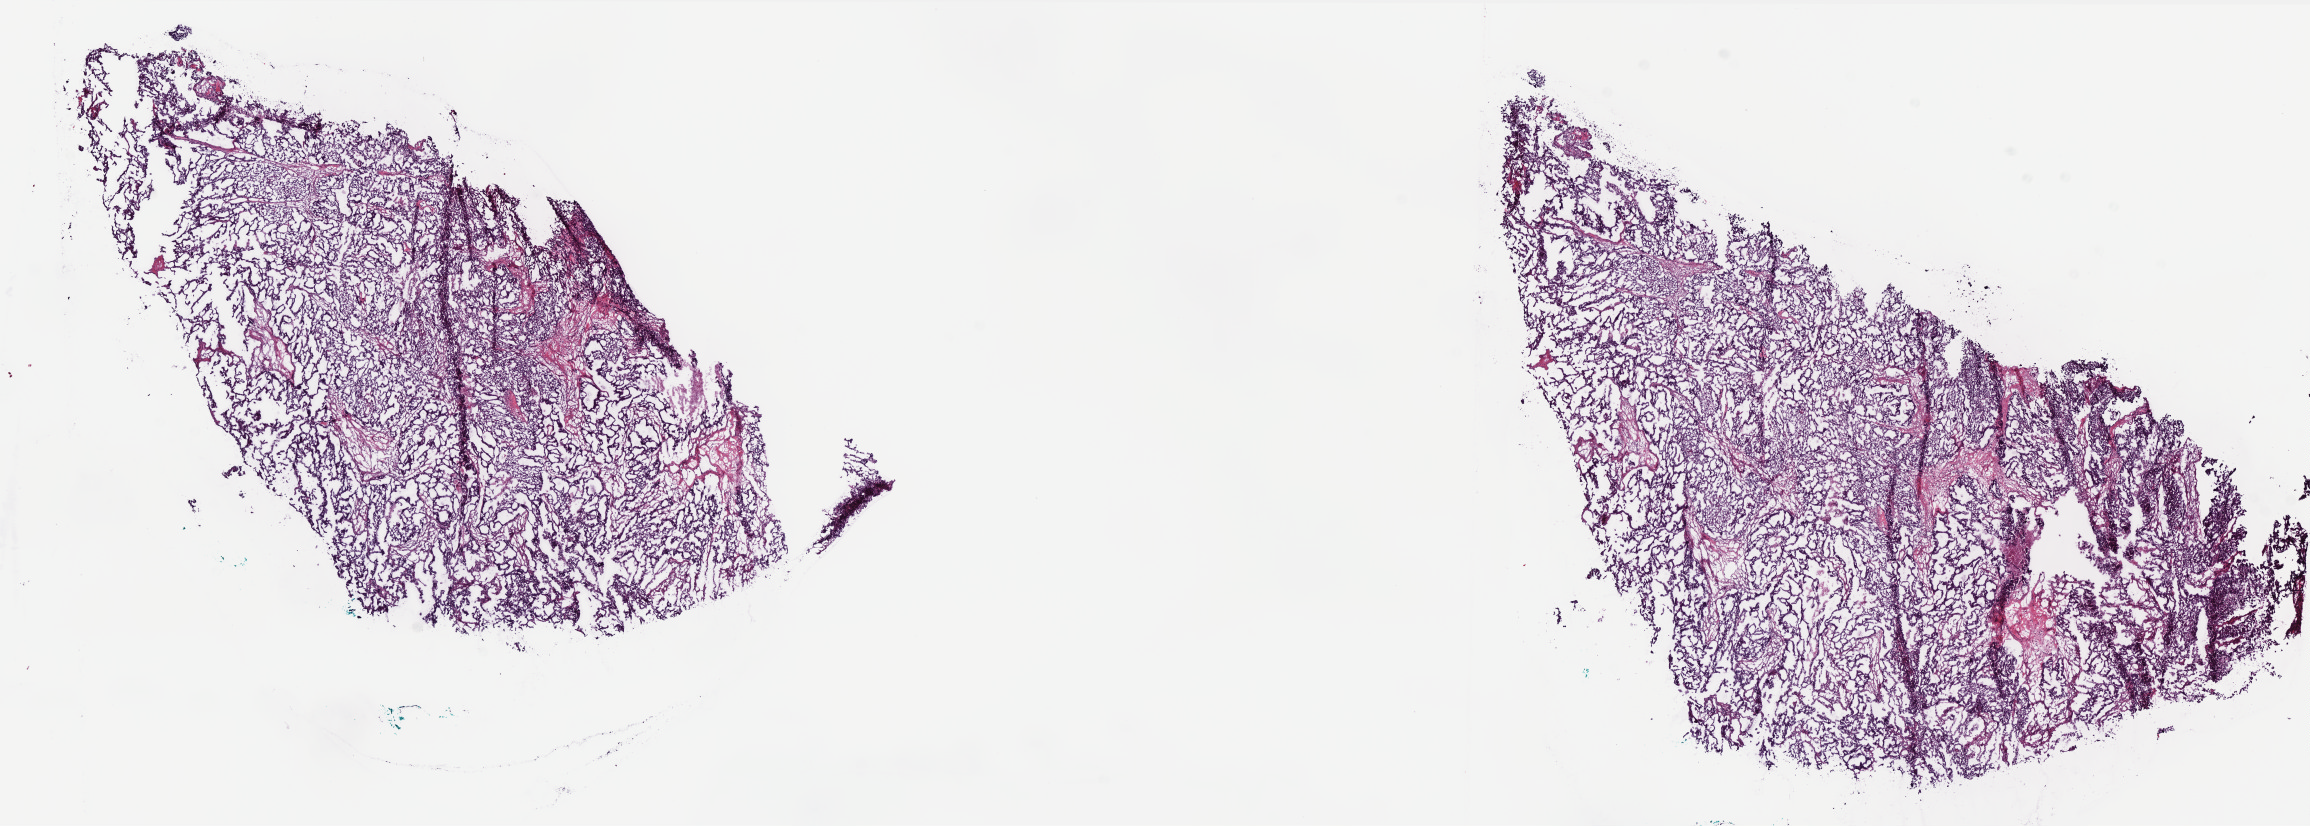
H&E-stained whole-slide image — a low-resolution overview of the entire scanned area, about 18.5 x 6.6 mm. Frozen section. Primary tumour sample from the uterus. Female, age 58 years at initial diagnosis. Histologic grade: G1 (well differentiated). Composition of this section per pathologist review: tumour cells 75%, tumour nuclei 75%, normal cells 0%, stromal cells 20%, necrosis 5%. Infiltration values recorded for this section: lymphocyte infiltration 20%, monocyte infiltration 5%, neutrophil infiltration 10%.
FIGO stage: IA. Histologic diagnosis: Endometrioid adenocarcinoma, NOS.